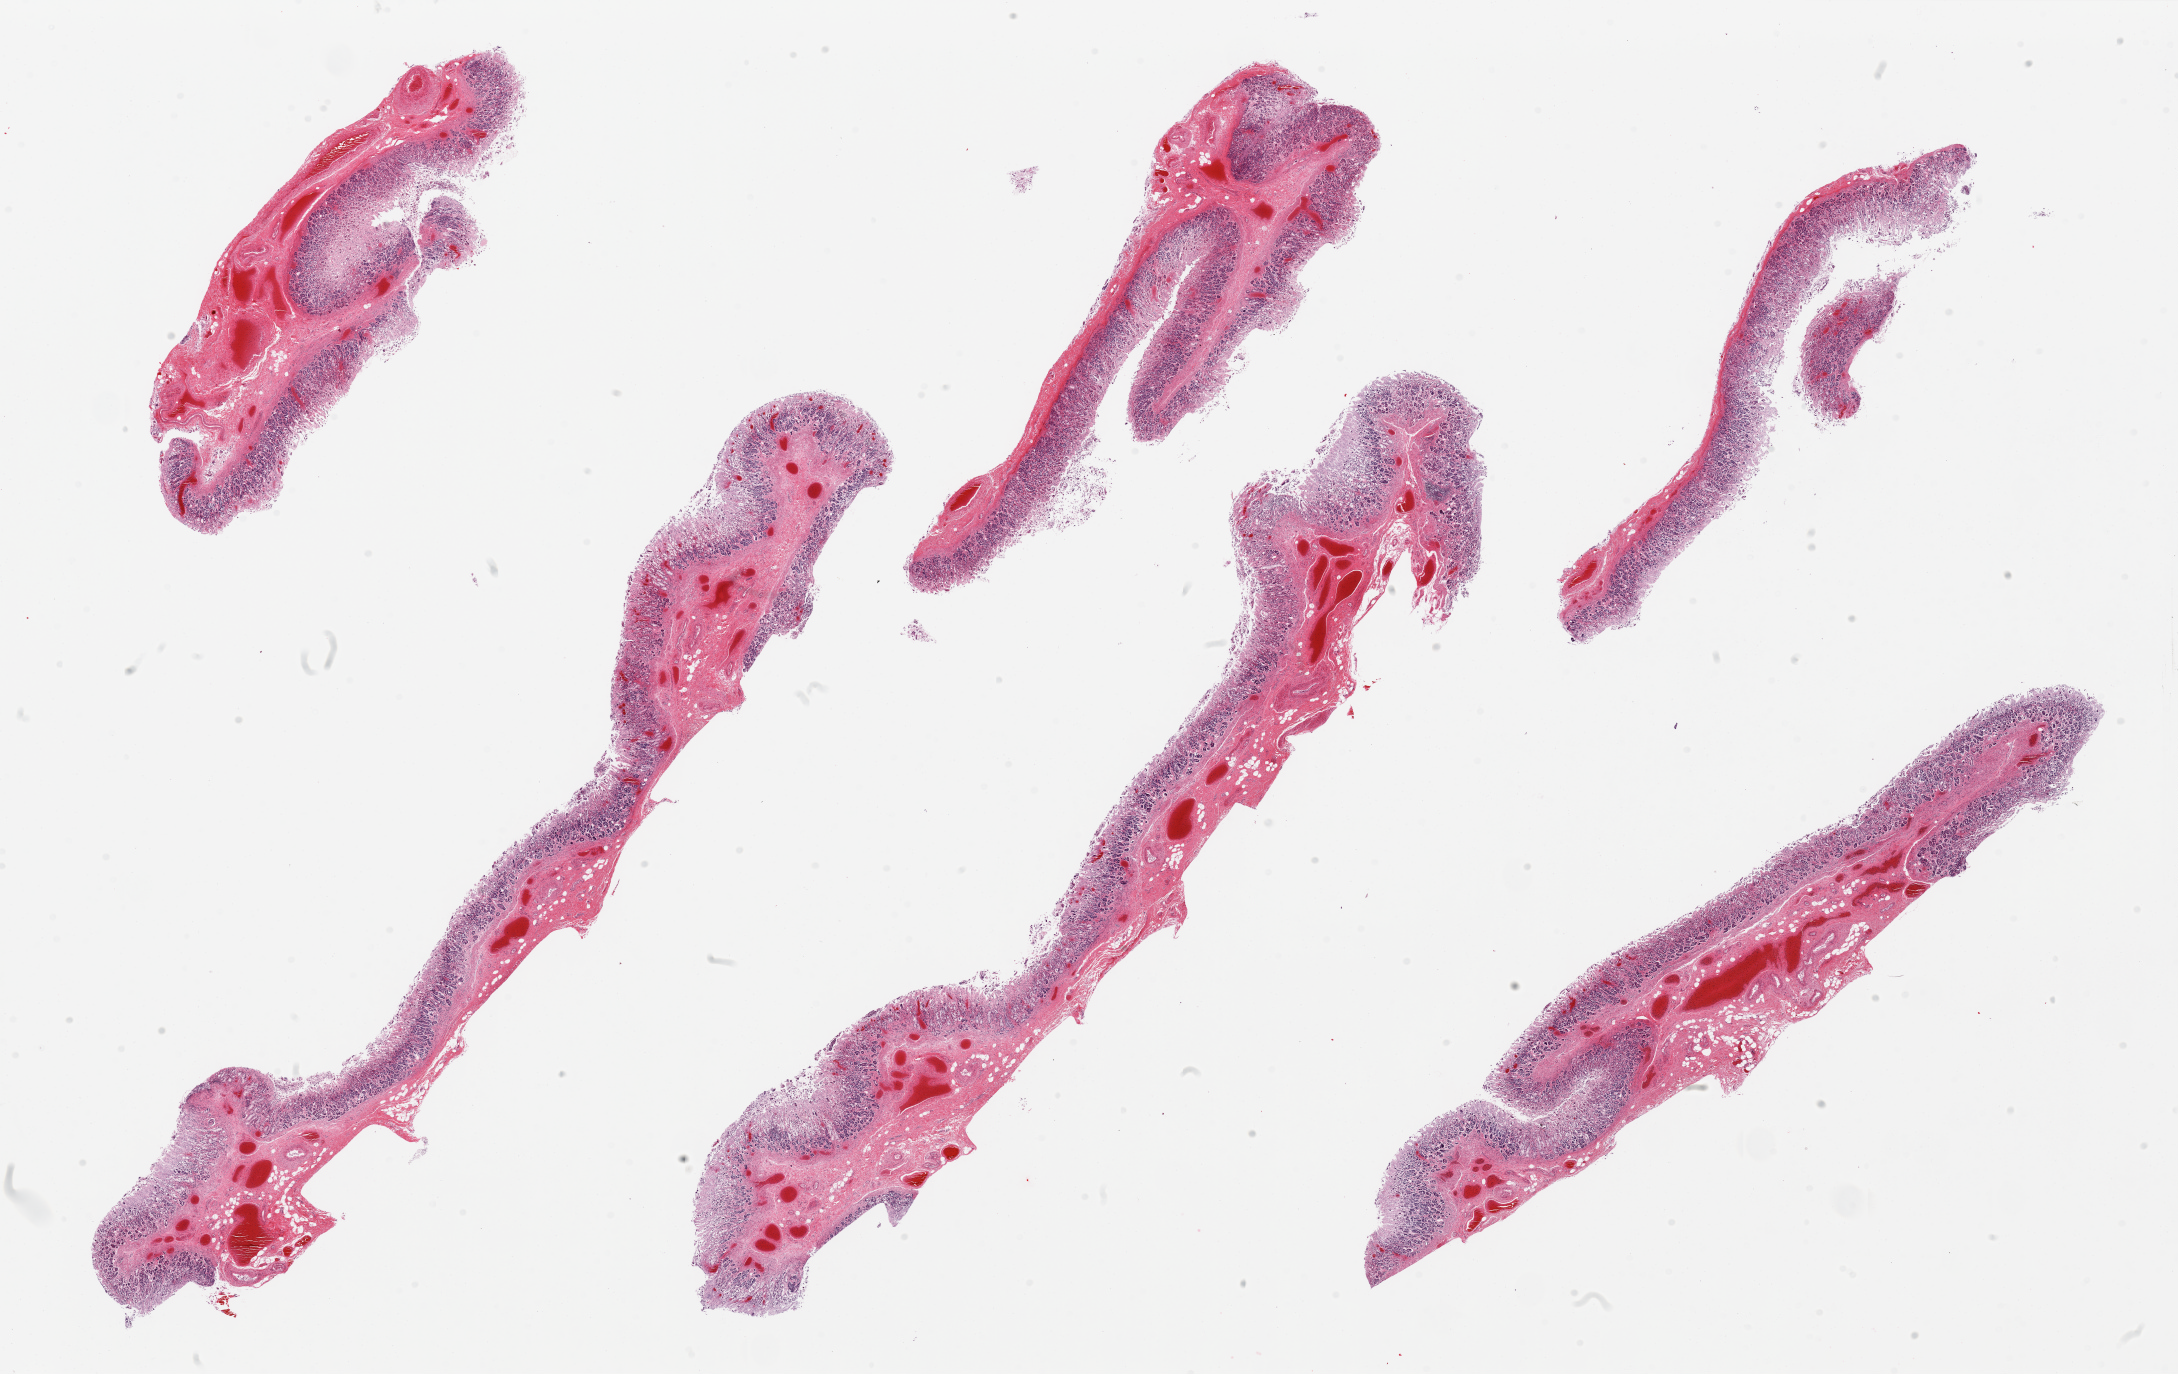
Hematoxylin and eosin (H&E) whole-slide image, whole scanned area (about 34.5 x 21.7 mm) shown as a low-resolution overview. PAXgene-fixed, paraffin-embedded tissue. Sampled site (target tissue): stomach. Donor tissue sample. Donor sex: female.
* reviewer comment on this tissue sample: 6 pieces, well dissected mucosa; some areas are severely autolyzed